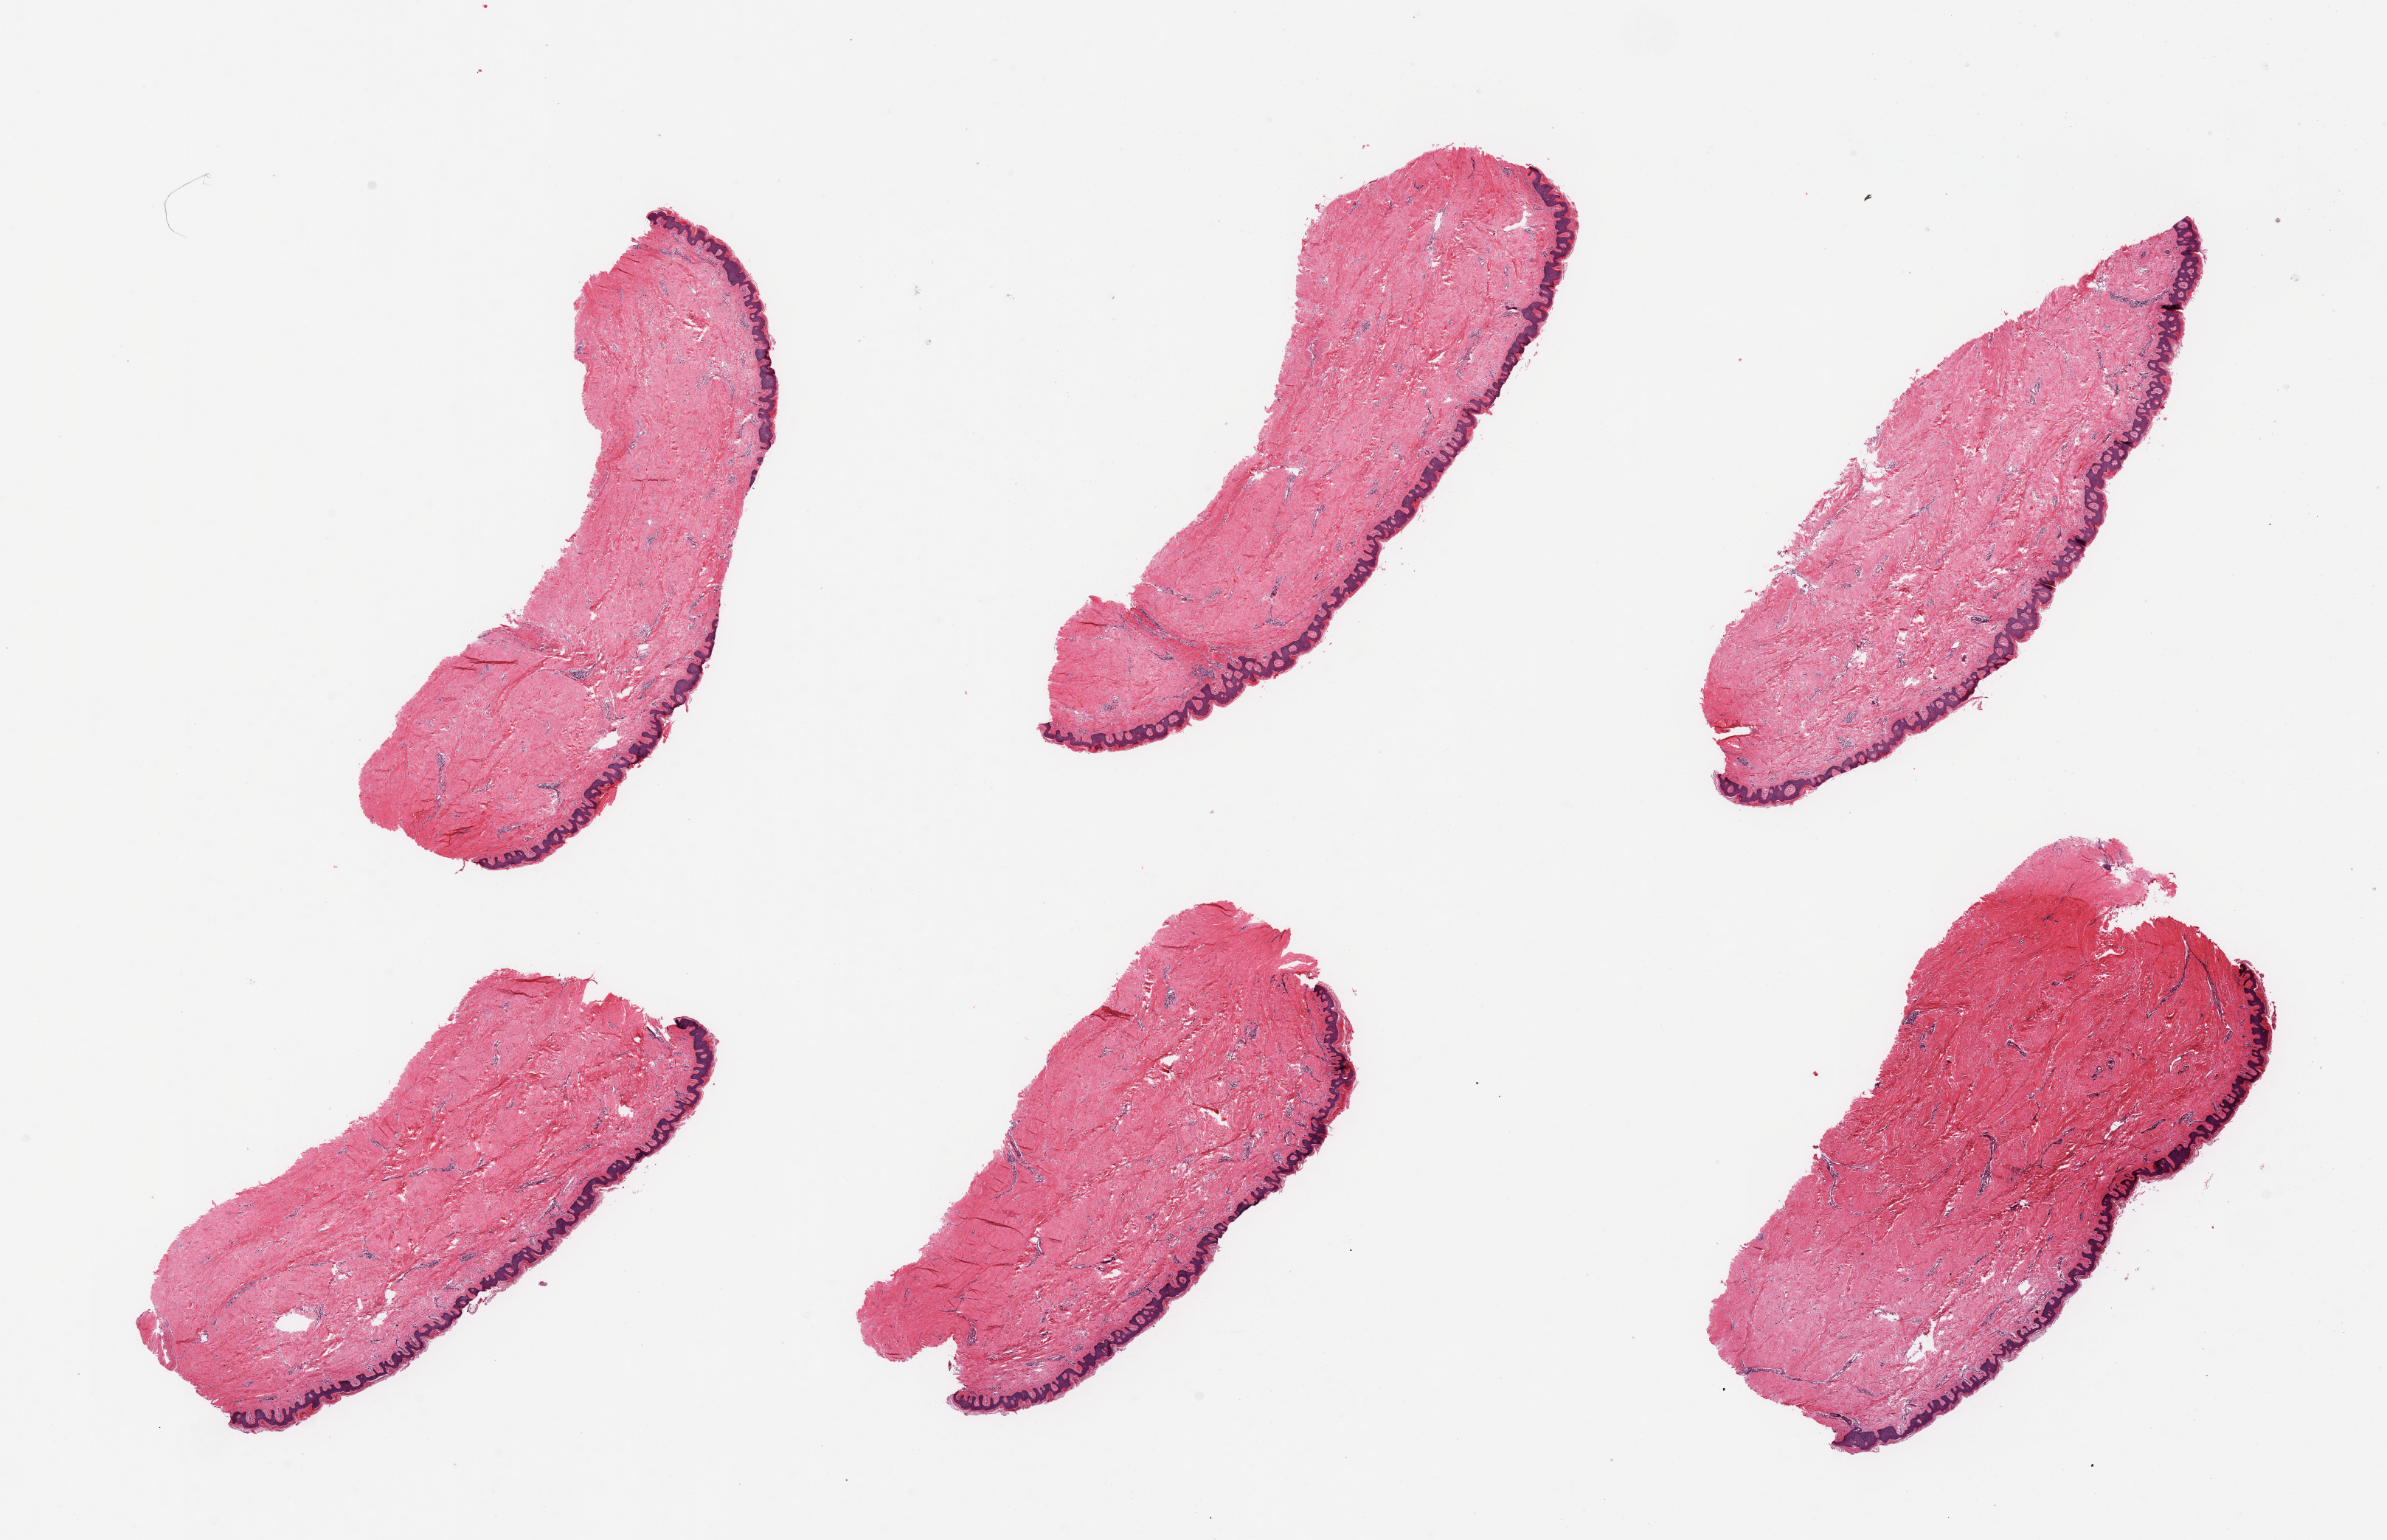
Digitized hematoxylin and eosin (H&E)-stained section — whole scanned area (about 25.6 x 16.5 mm) shown as a low-resolution overview; PAXgene-fixed paraffin-embedded (PFPE) section; target tissue: skin of suprapubic region; tissue donor sample. Male donor.
Review note (as recorded): 6 pieces, no significant dermal fat; squamous epithelium is ~60-70 microns.